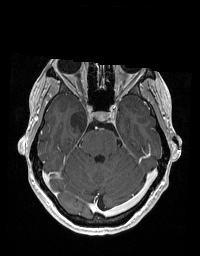
Brain MRI from a brain-tumour surgery series, one axial slice; position 126 of 192 along the scan axis; T1-weighted post-contrast; 1 mm slice thickness; 200 × 256 image matrix. Case-level facts recorded for this patient, not image findings: histopathology: Glioblastoma; WHO grade: 2; IDH mutation: no; tumour location: Right Skull Base Temporal.
Outlined on this slice (expert manual segmentation):
- tumour: bounding box <71,111,100,132> (left, top, right, bottom; pixels)